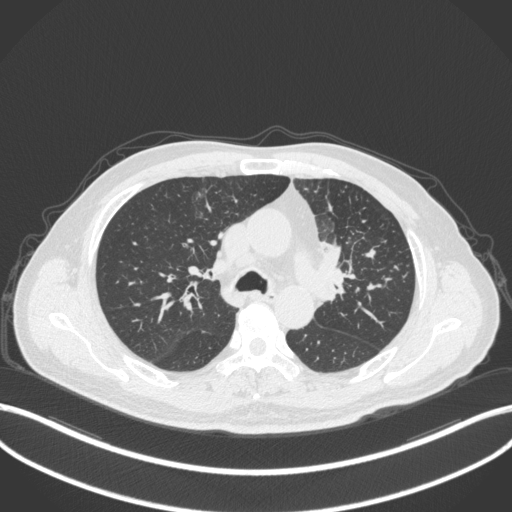
Chest CT, one axial slice; position 229 of 386 along the scan axis; reconstruction kernel B31f; lung window (W 1500 / L -600 HU); 512 × 512 image matrix, field of view 400 × 400 mm. Male patient, age 69 years. Case-level facts recorded for this patient, not image findings: clinical TNM (as recorded): T2a N2 M0.
Structures marked on this image (rectangle marked by the reading radiologist):
- lung tumour (recorded histology: adenocarcinoma): box from (x=321, y=239) to (x=357, y=290) px